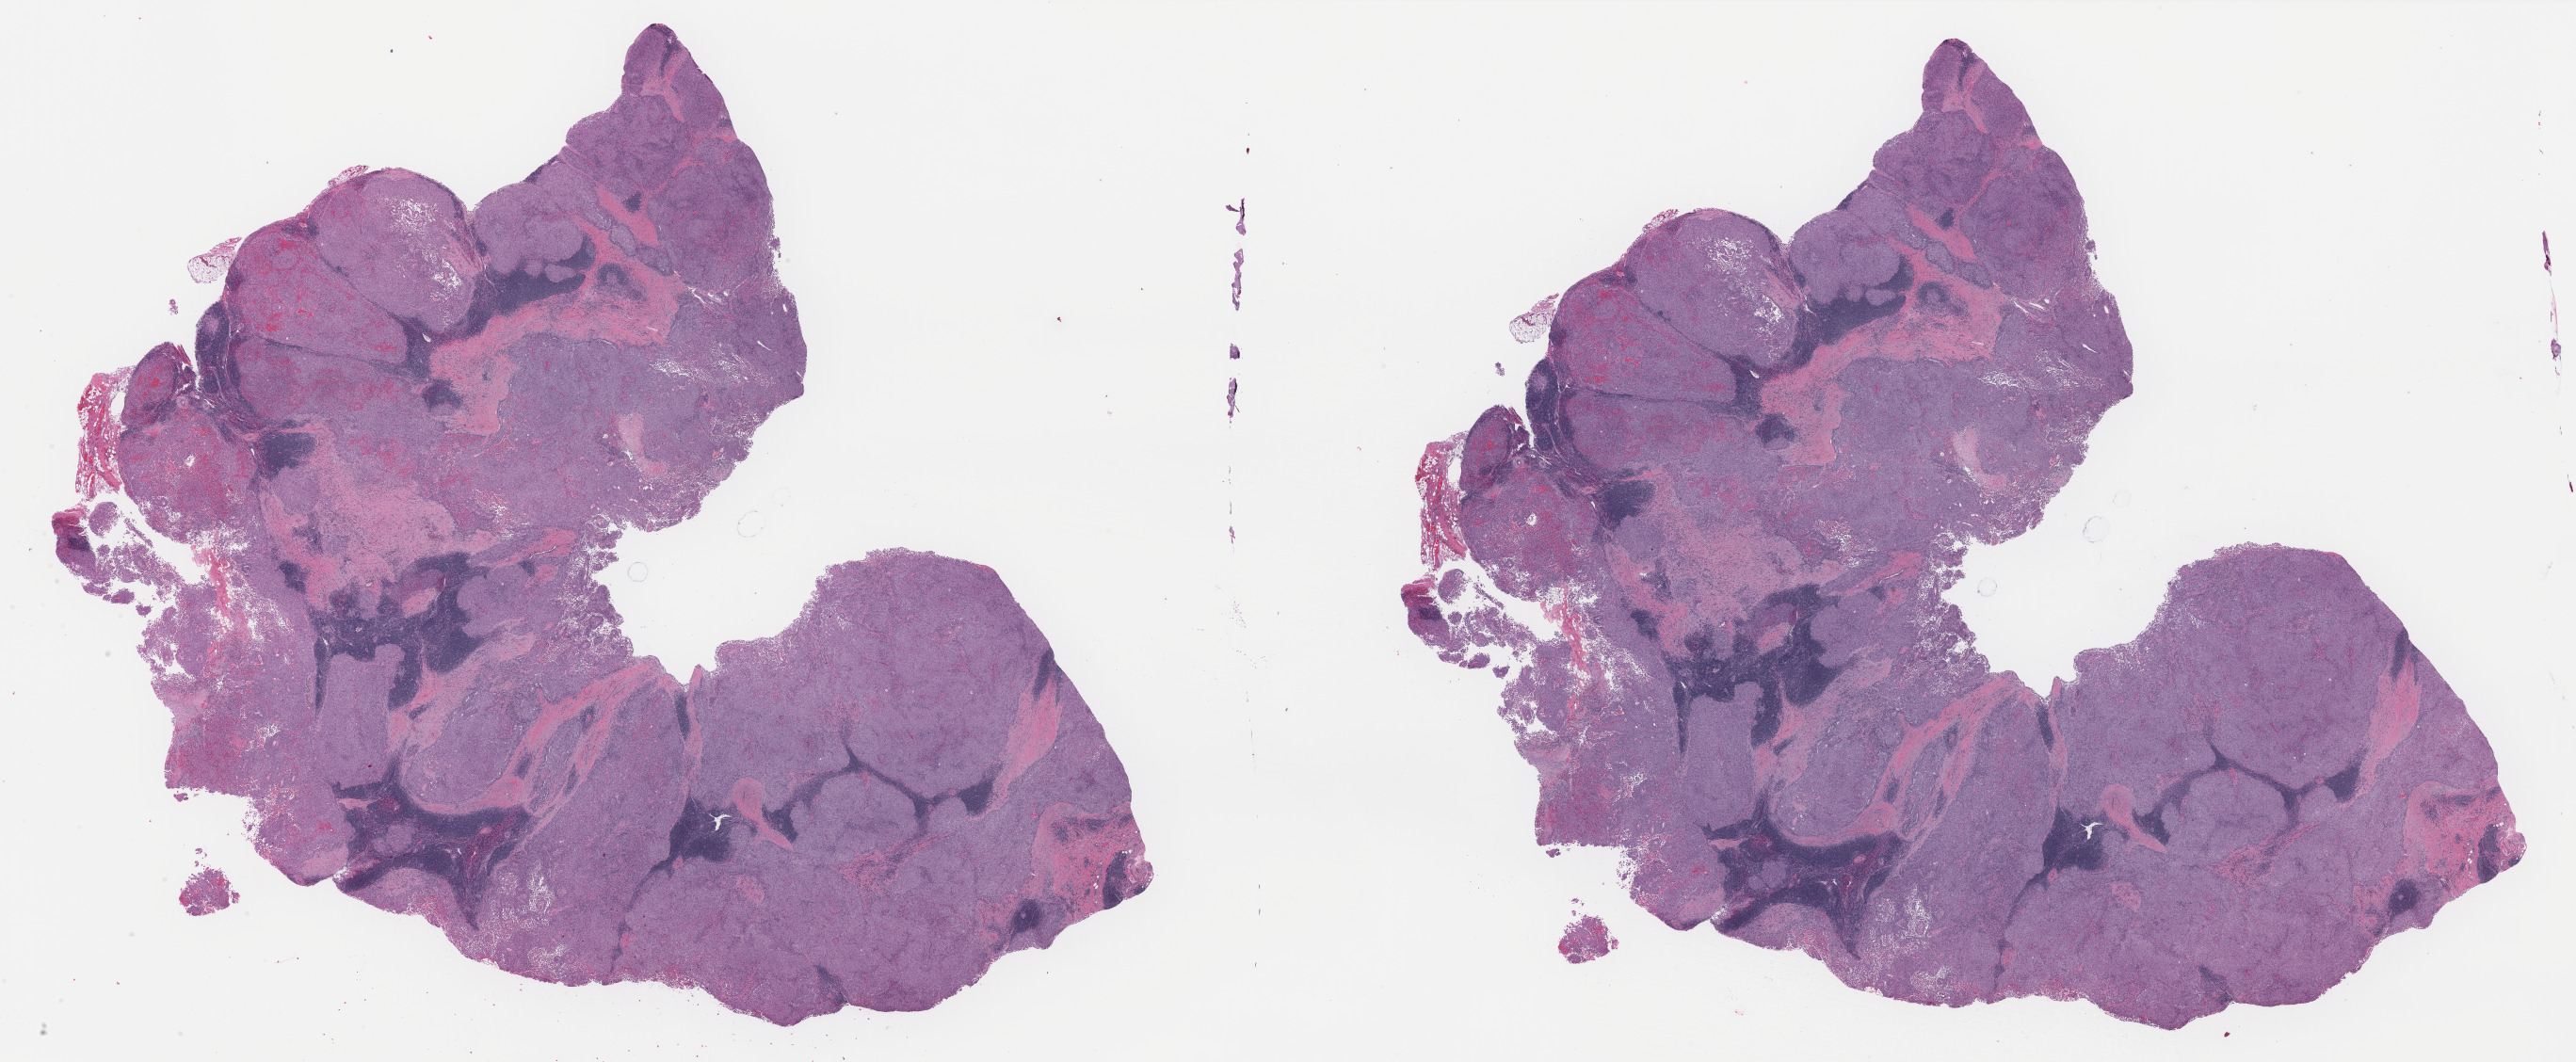
Digitized Hematoxylin and eosin (H&E) stained tissue section (whole slide) — low-resolution overview of the scanned area, about 43.3 x 17.9 mm, formalin-fixed paraffin-embedded (FFPE) diagnostic section, metastatic tumour sample, sampled site: lymph nodes of axilla or arm. Patient: male, age at initial diagnosis 41 years.
This section: metastatic tumour tissue. Patient diagnosis: Malignant melanoma, NOS.